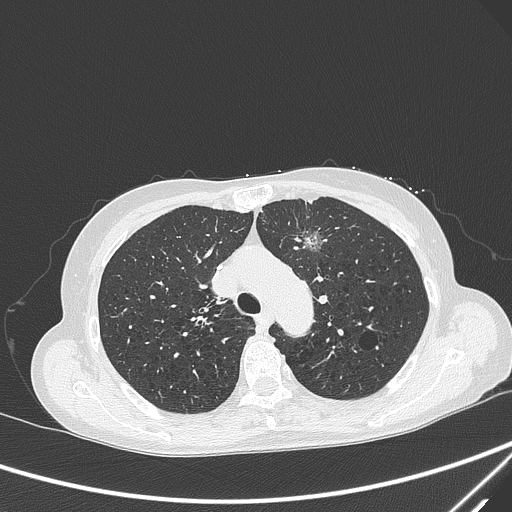
Chest CT, one axial slice; position 219 of 299 along the scan axis; 120 kVp; lung window (W 1500 / L -600 HU); 1 mm slice thickness; 512 × 512 image matrix, field of view 350 × 350 mm. Patient: female, 71 years. Case-level facts recorded for this patient, not image findings: clinical TNM (as recorded): T1c N0 M0; histopathological grade: G2-3.
Annotated regions visible in this slice (rectangle marked by the reading radiologist):
- lung tumour (recorded histology: adenocarcinoma): box from (x=292, y=222) to (x=326, y=254) px